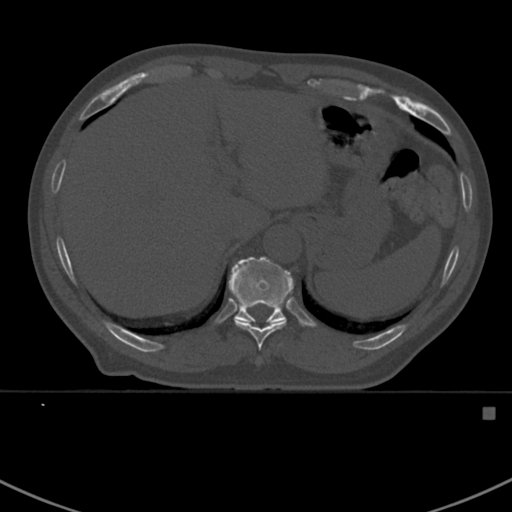
CT including the spine, one axial slice. 120 kVp. Bone window (W 1800 / L 400 HU). 1.5 mm slice thickness. 512 × 512 image matrix, field of view 358 × 358 mm. Patient: male, 59 years. Case-level facts recorded for this patient, not image findings: primary cancer: prostate.
Outlined on this slice (semi-automatically segmented with operator editing):
- T10 vertebra: bounding box <234,305,286,364> (left, top, right, bottom; pixels)
- T11 vertebra: <228,257,294,324>